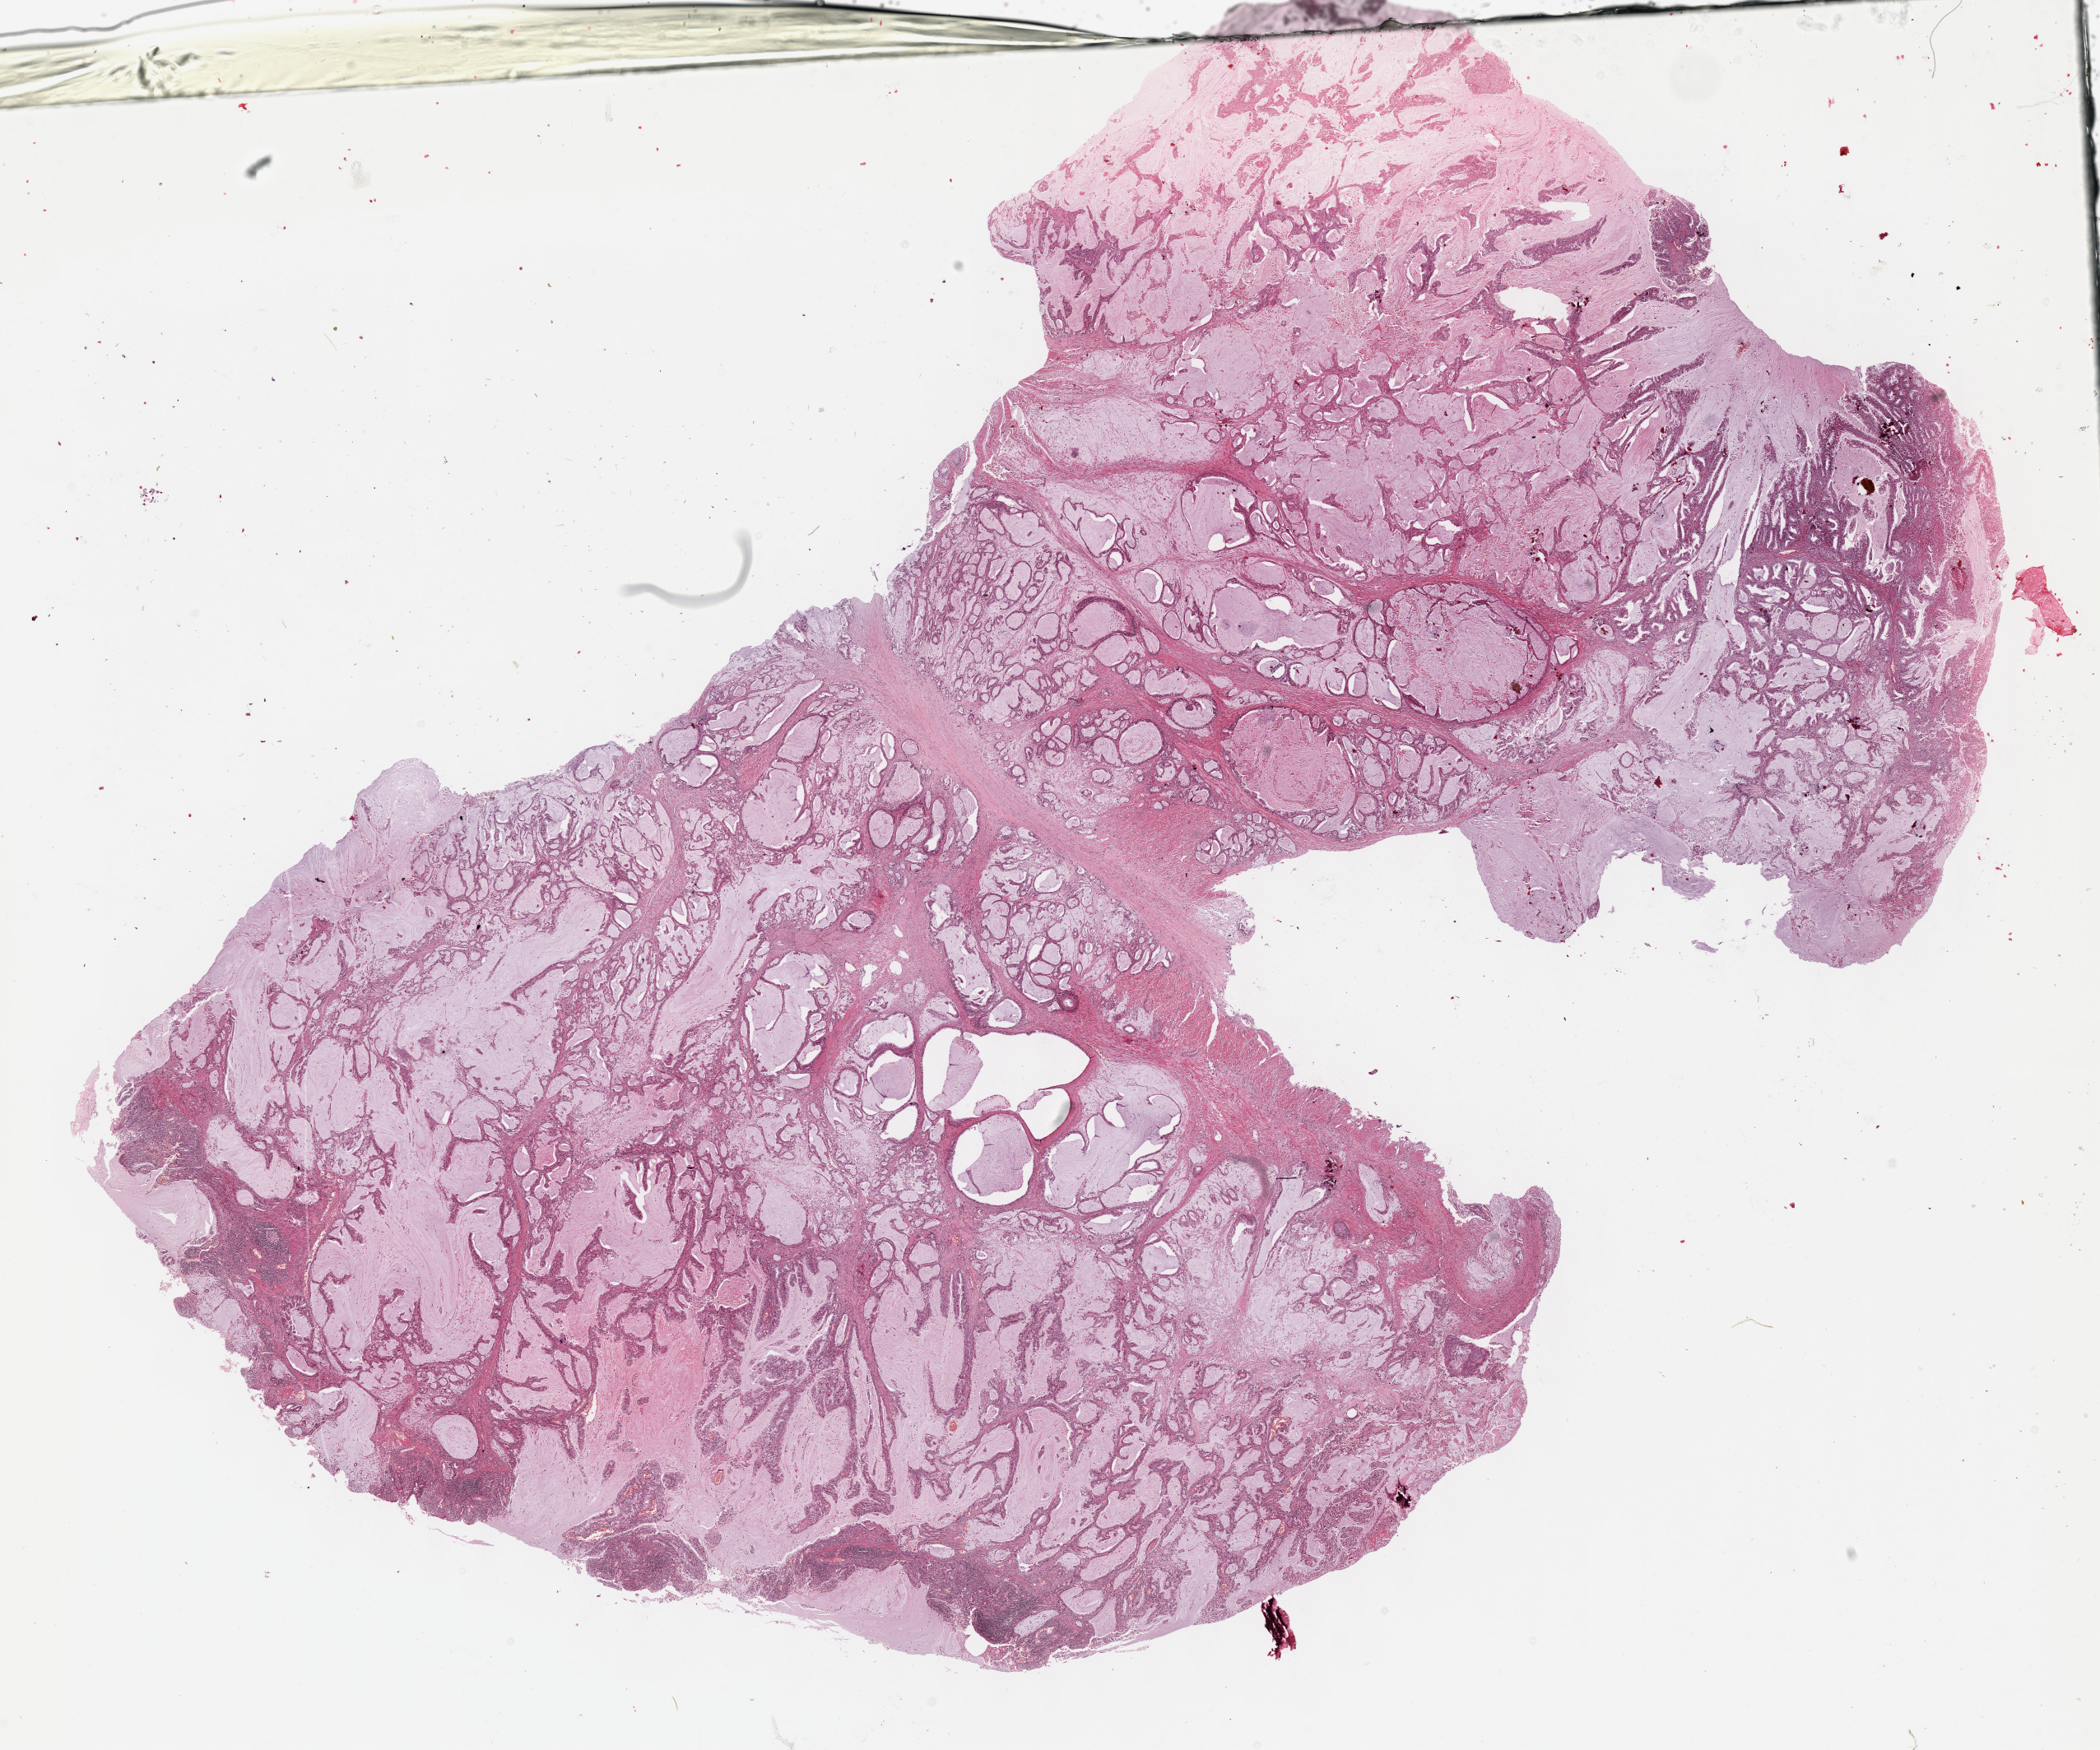
Digitized H&E tissue section (whole slide), low-resolution overview of the scanned area, about 20.6 x 17.2 mm (acquisition: 40x scan), formalin-fixed paraffin-embedded (FFPE) diagnostic section, primary tumour sample from the stomach. Male, age 65 years at initial diagnosis. Histologic grade: G2 (moderately differentiated).
* AJCC pathologic stage: IV
* TNM: T4 N0 M1
* pathologic diagnosis: Mucinous adenocarcinoma